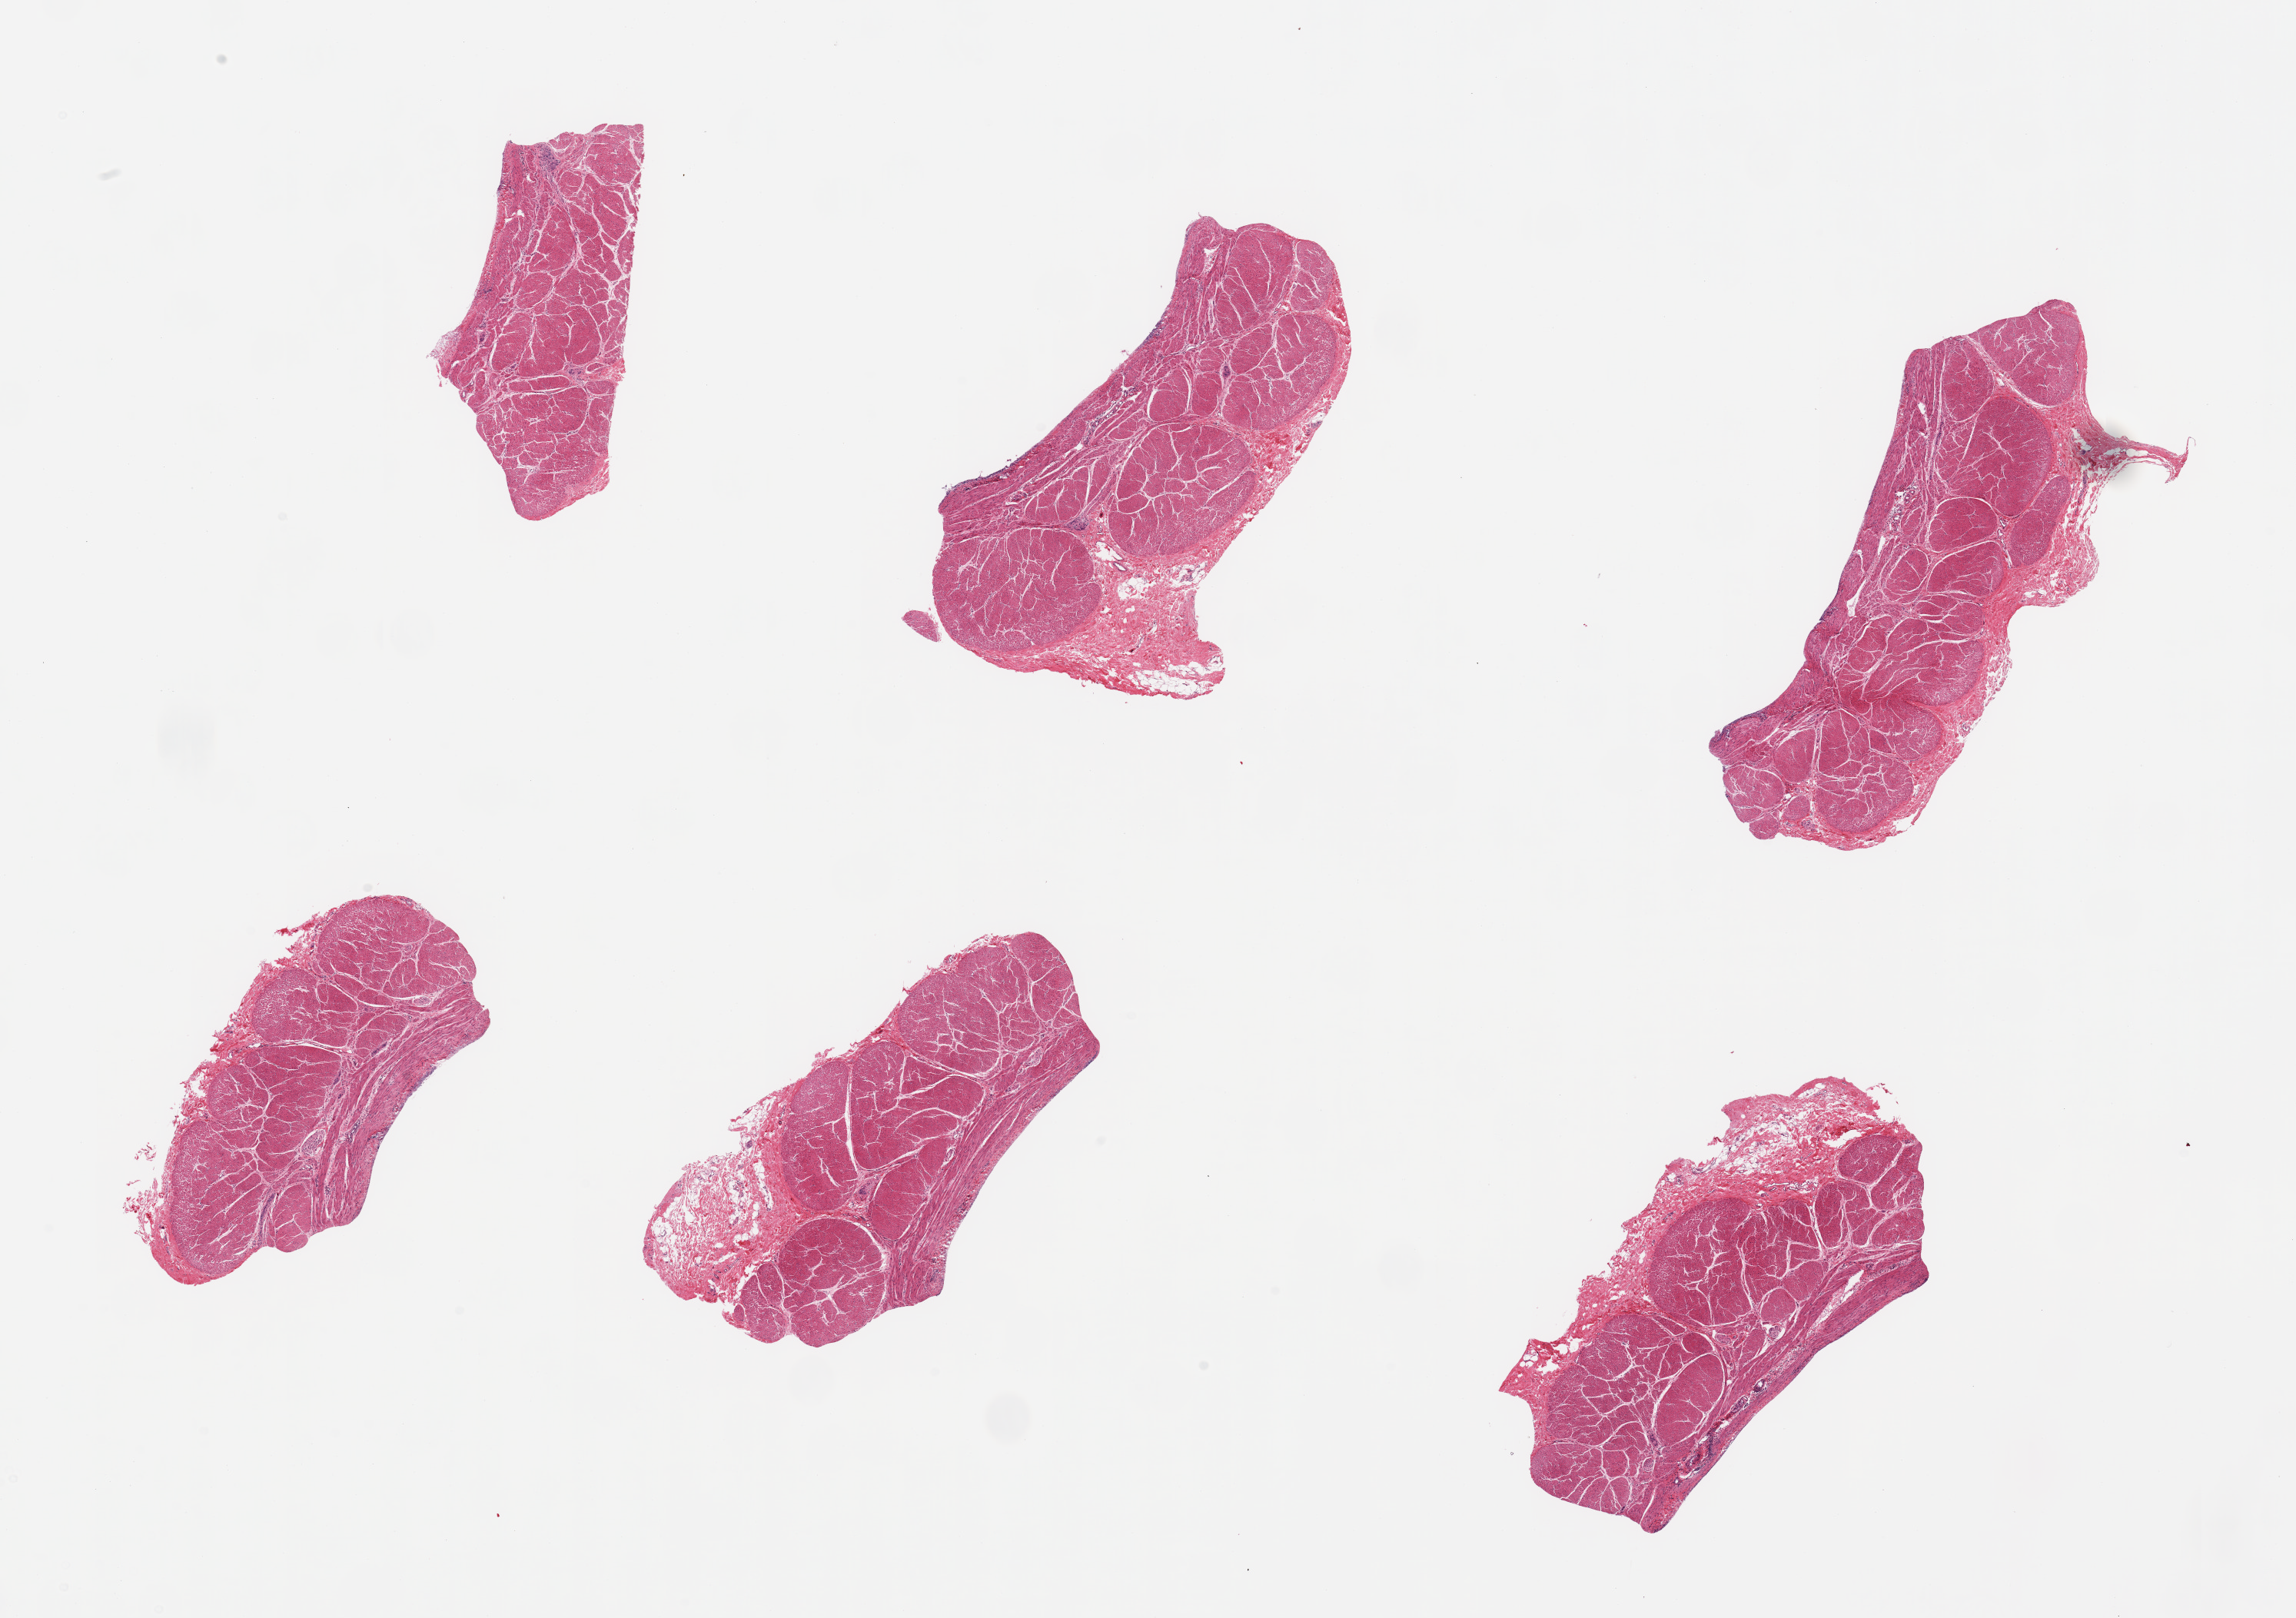
Digitized H&E-stained section, brightfield — a low-resolution overview of the entire scanned area, about 23.6 x 16.6 mm (slide scanned at 20x), PAXgene-fixed paraffin-embedded (PFPE) section, section of stomach (target tissue), tissue donor sample. Donor: male.
Pathologist's review note for this sample: 6 pieces, muscularis only, no mucosa.